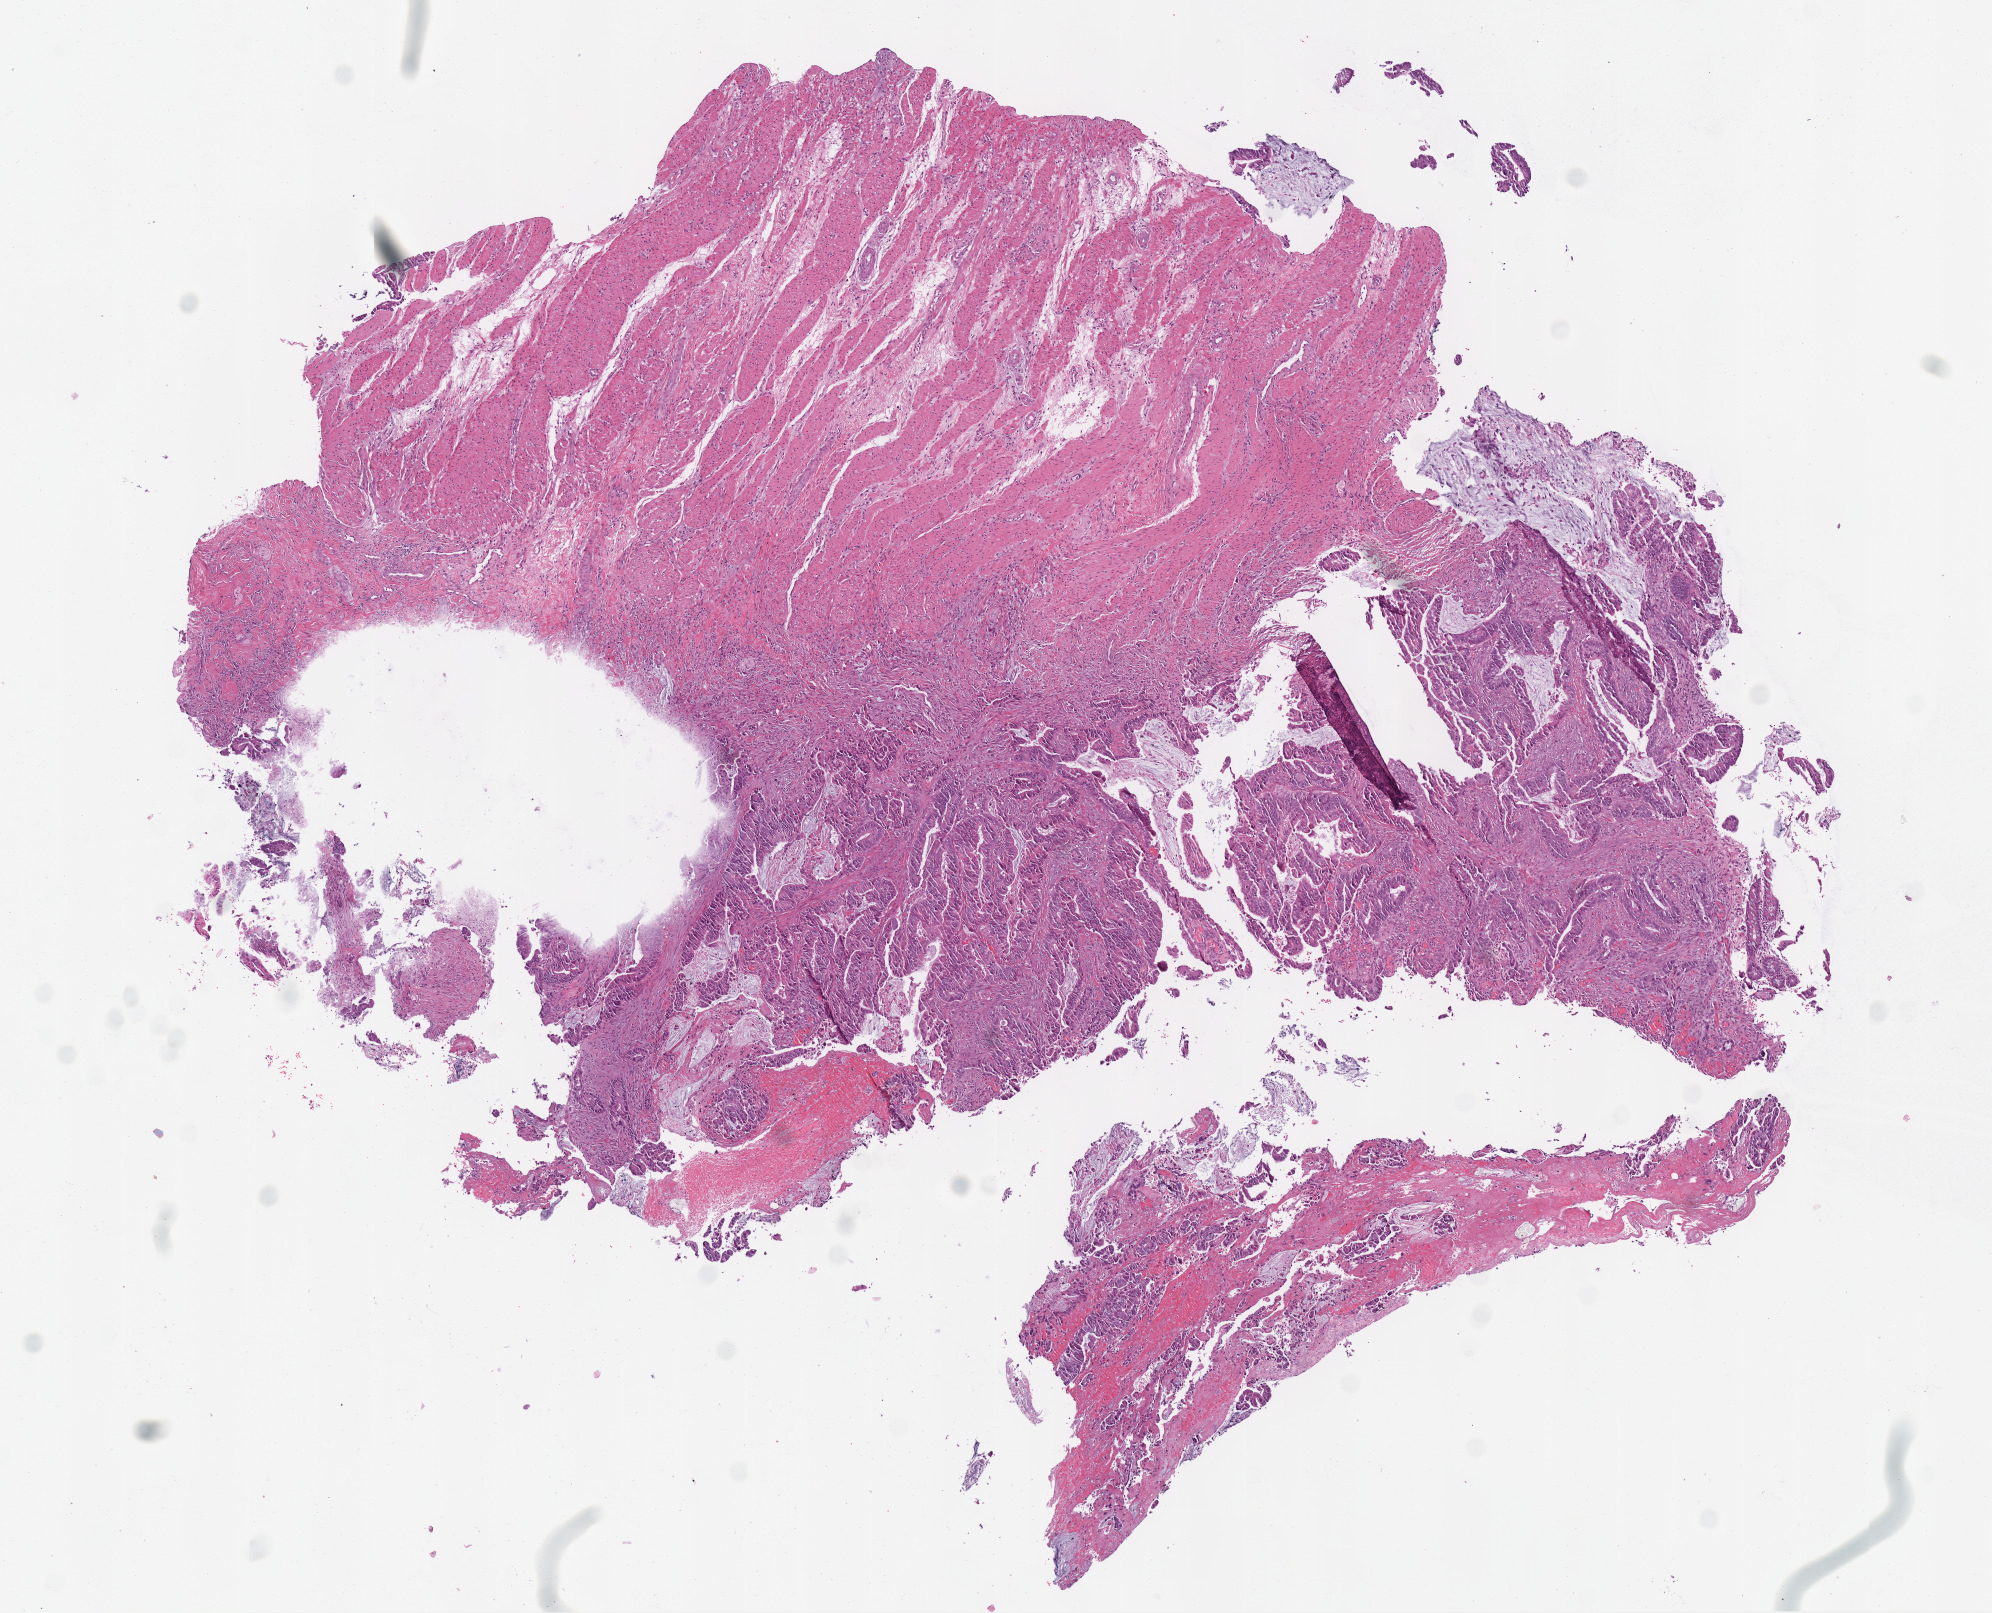
Whole-slide histology image, Hematoxylin and eosin (H&E) stained — a low-resolution overview of the entire scanned area, about 7.8 x 6.3 mm (from a 40x scan); frozen section from the top of the tissue portion; colon, primary tumour sample. Female, age 73 years at initial diagnosis. Pathologist review of this section (percent, as recorded): tumour cells 40%, tumour nuclei 75%, normal cells 50%, stromal cells 10%, necrosis 0%.
• AJCC pathologic stage: IIA (6th edition)
• histologic diagnosis: Adenocarcinoma, NOS